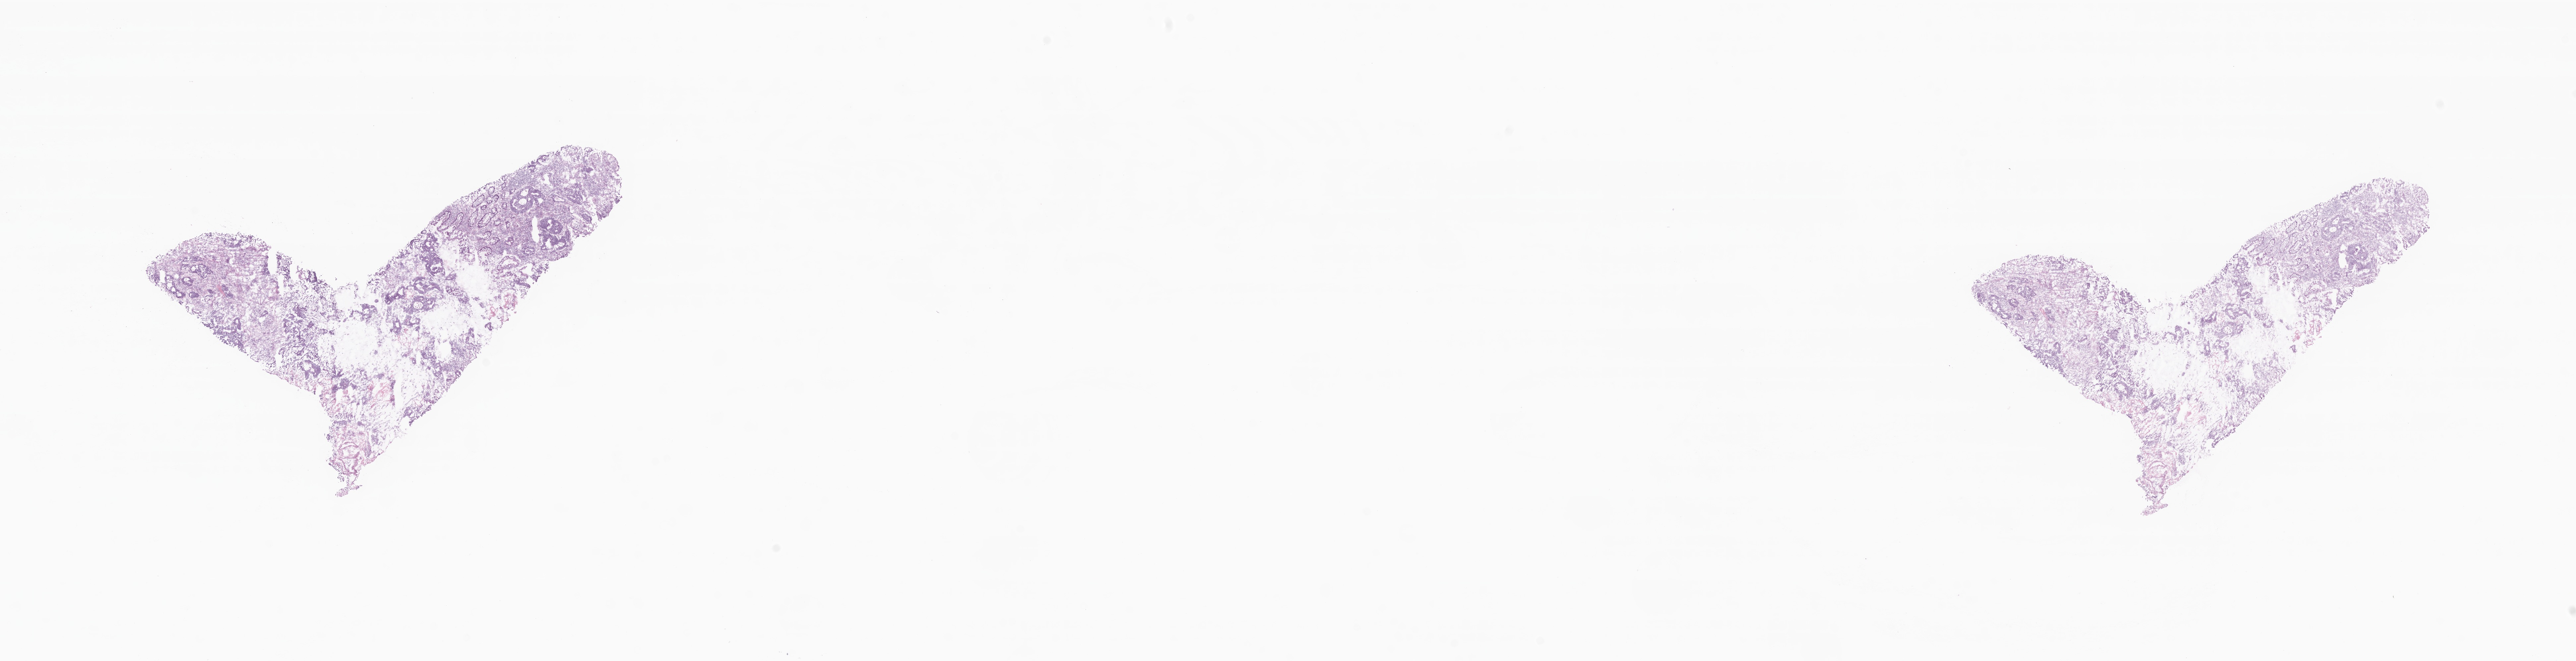
Digitized haematoxylin and eosin-stained section, whole scanned area (about 32.8 x 8.4 mm) shown as a low-resolution overview; frozen section (tissue freezing medium); specimen: primary tumor; anatomic site: cecum. Patient: male, age at initial diagnosis 72 years. Composition of this section per pathologist review: tumor cells 29%, tumor nuclei 40%.
Diagnosis: Adenocarcinoma, NOS.